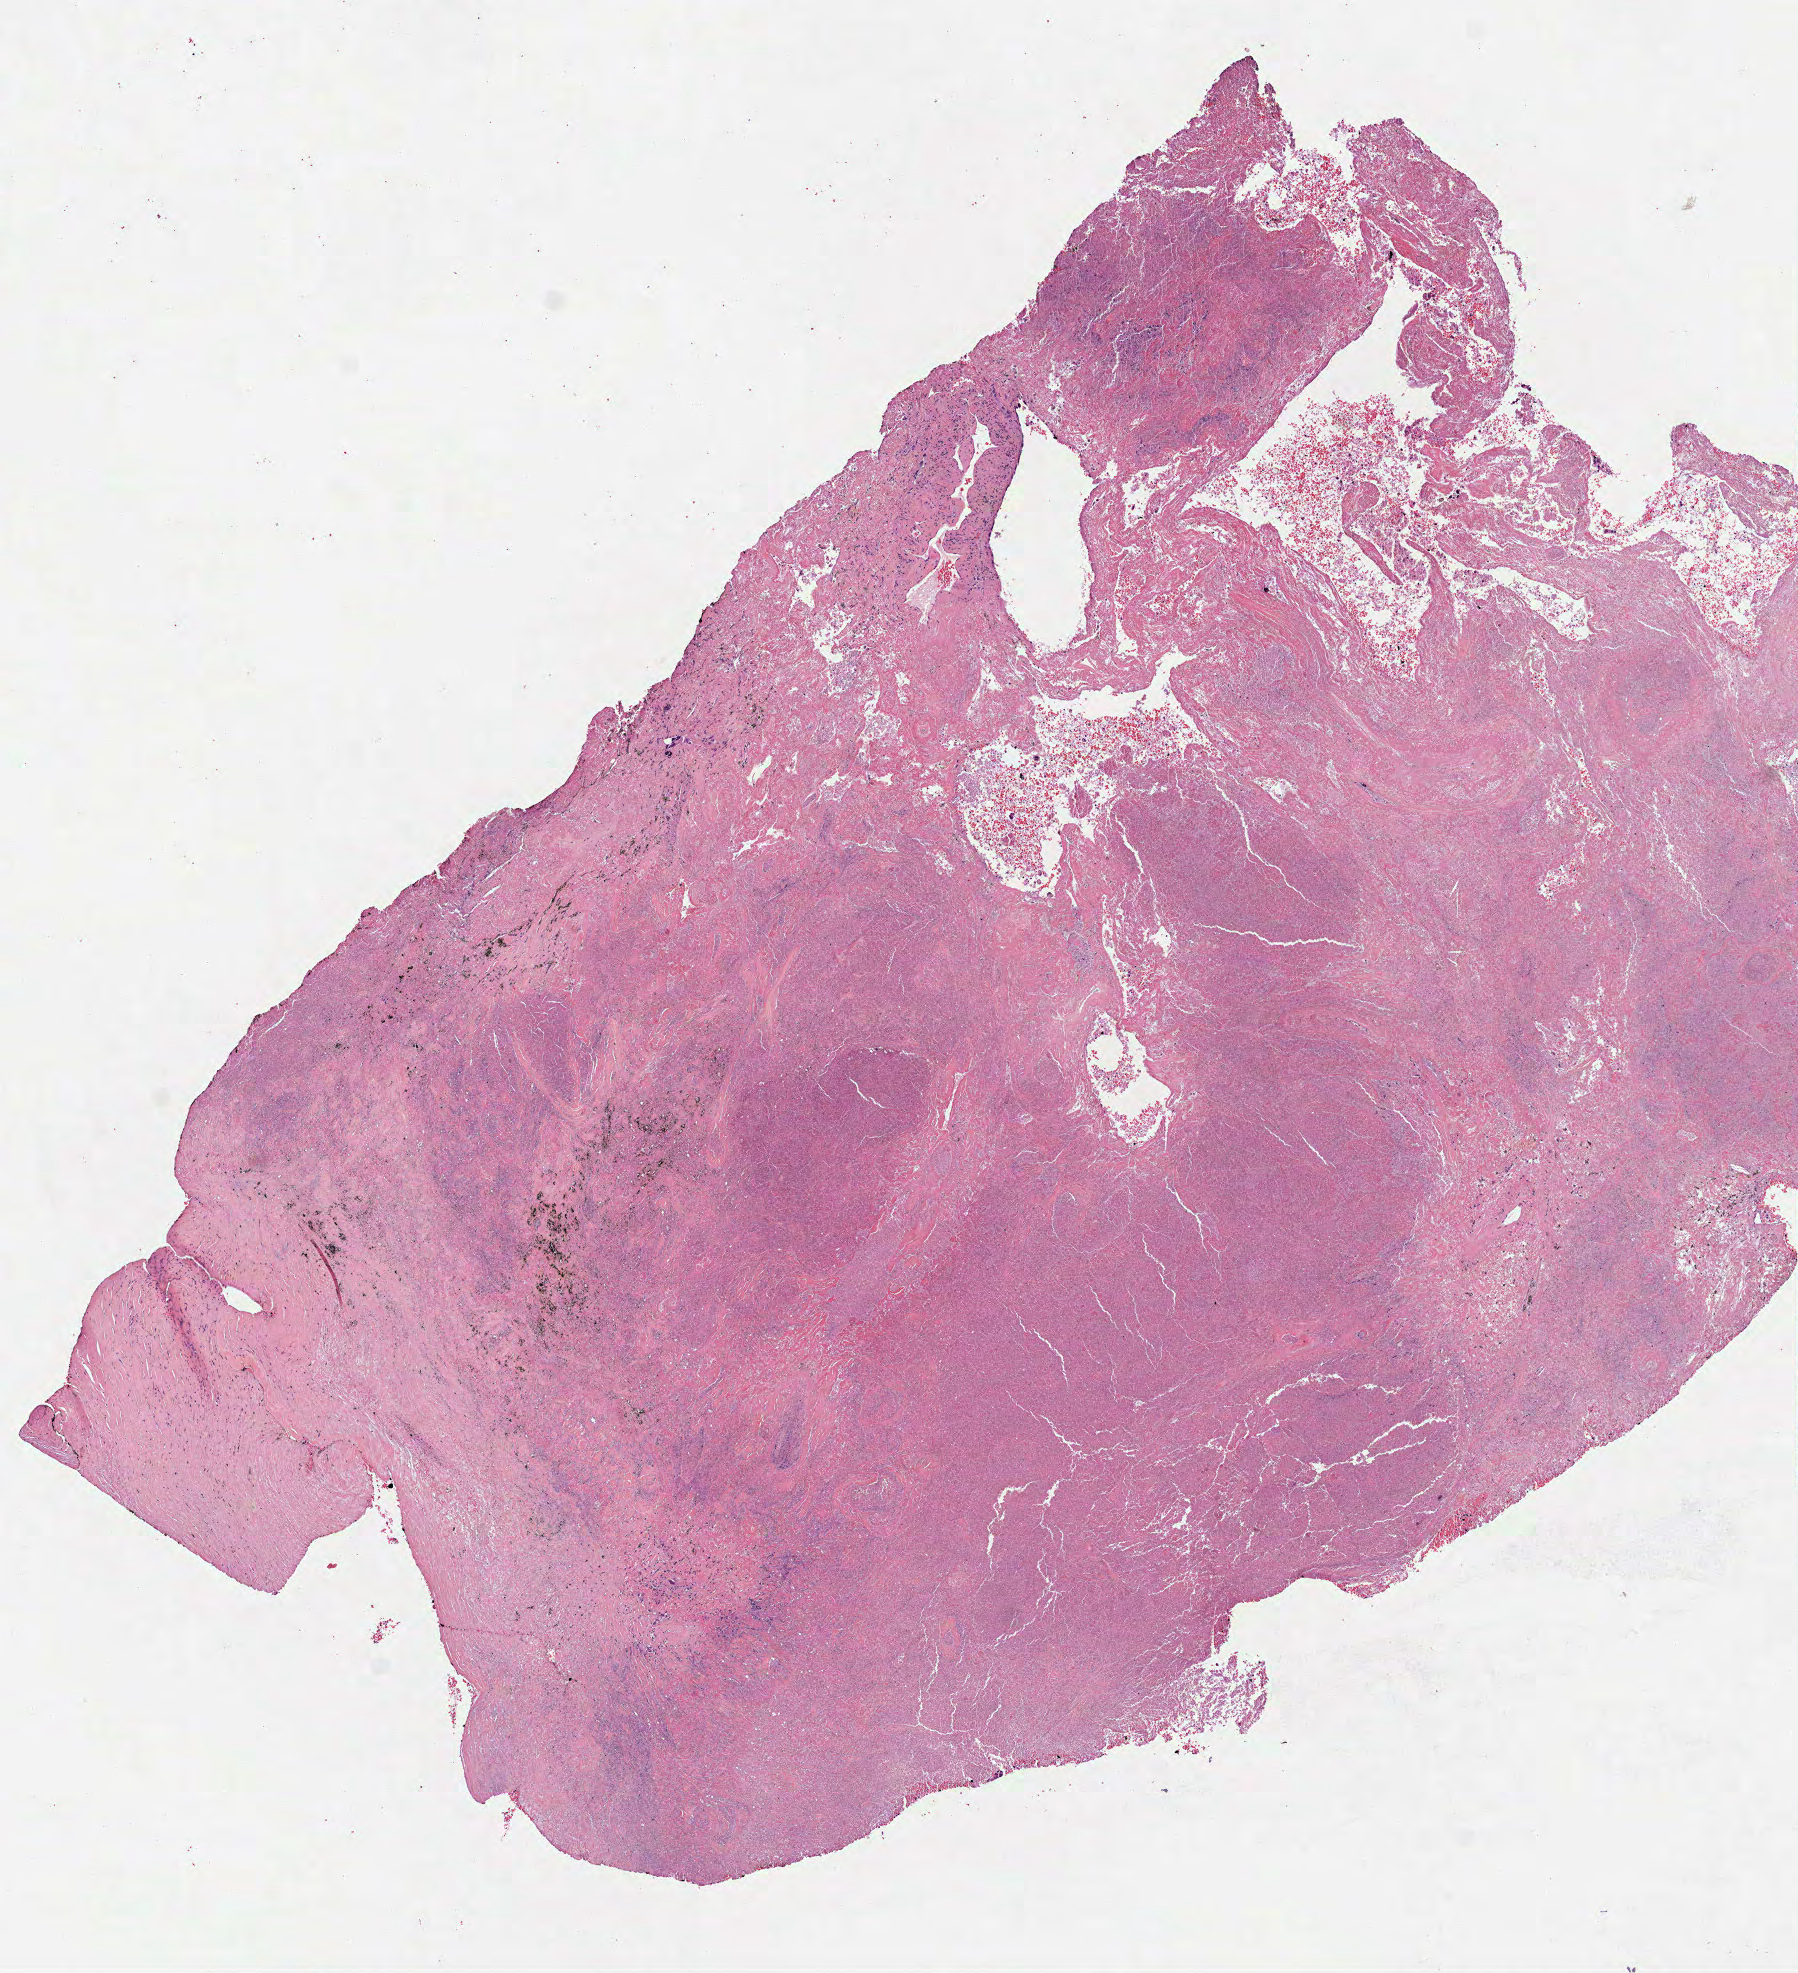
Whole-slide histology image, H&E, shown as a low-resolution overview of the whole scanned area (about 7.3 x 8.0 mm, slide scanned at 40x); FFPE section; primary tumour sample from the lung. Male patient; age at initial diagnosis 71 years.
AJCC pathologic stage: IIA. Histologic diagnosis: Adenocarcinoma, NOS (upper lobe, lung). TNM: T2a N1 MX.